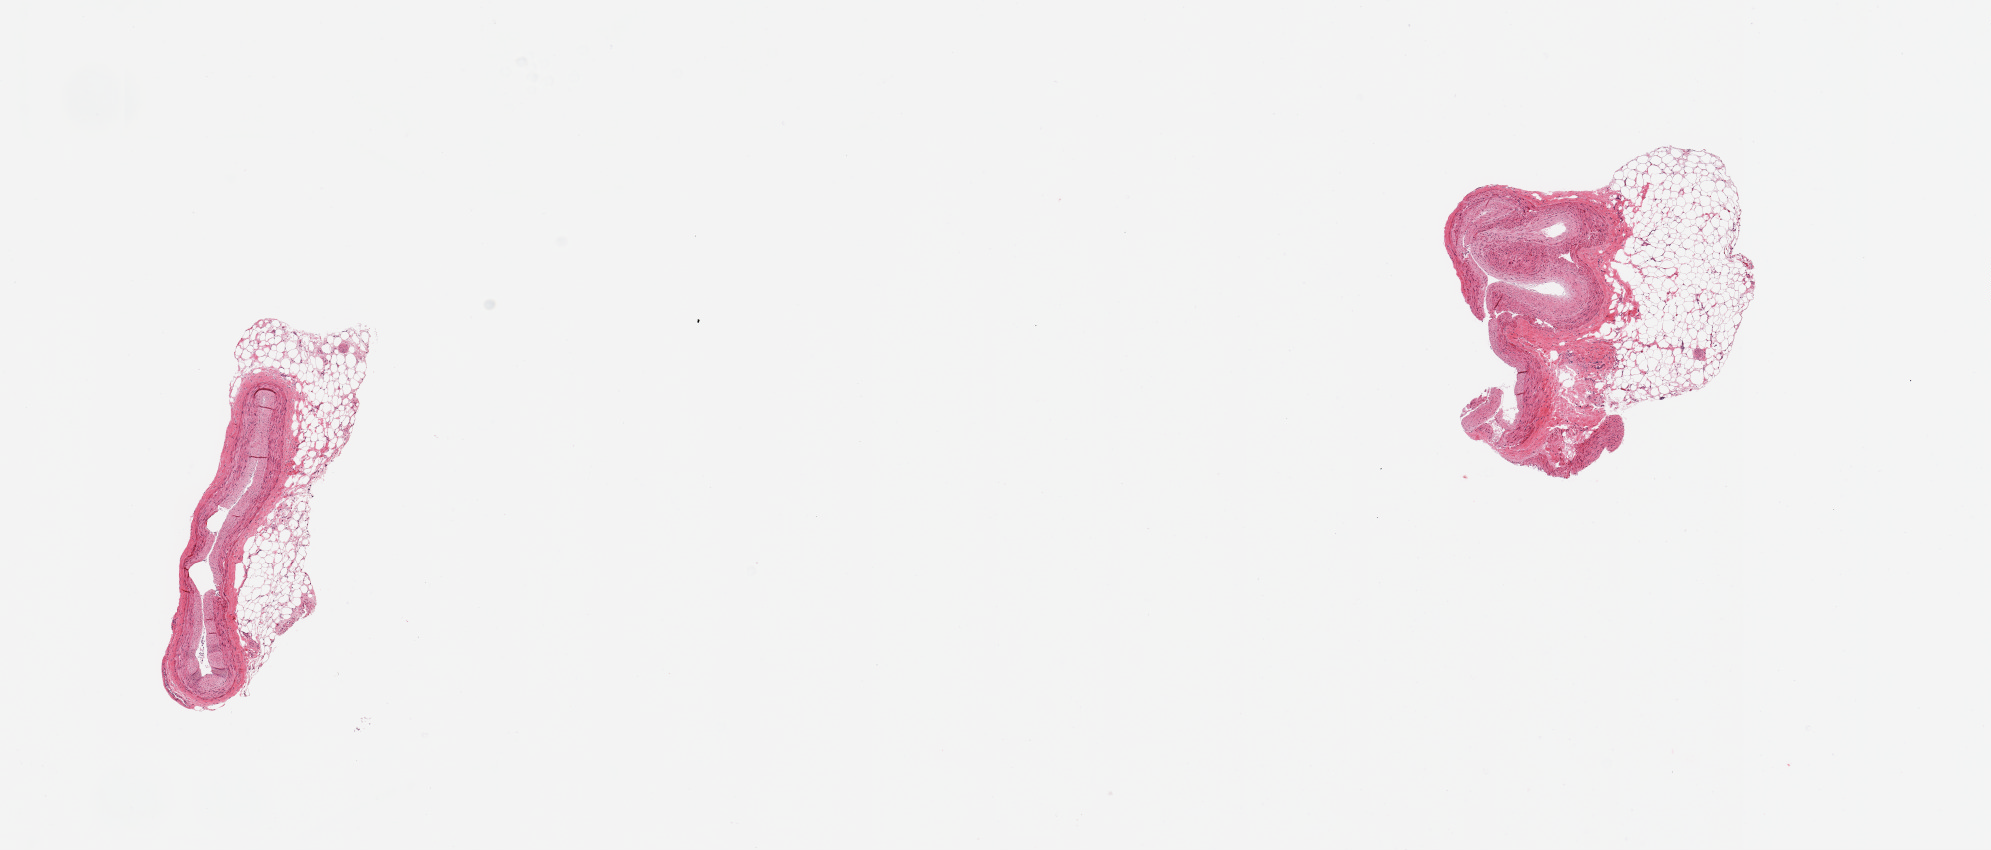
Whole-slide image, H&E stain, brightfield, low-resolution overview of the scanned area, about 15.8 x 6.7 mm, PAXgene-fixed, paraffin-embedded tissue, sampled site (target tissue): coronary artery, tissue donor sample. Donor sex: male.
Review note (as recorded): 2 pieces; artery with attachment of fat (40-50%).